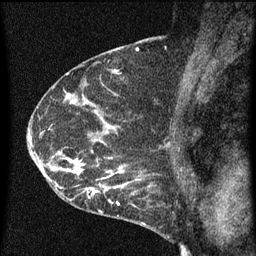
Breast MRI (dynamic contrast-enhanced), one sagittal slice; position 42 of 60 along the scan axis; dynamic contrast-enhanced series, image 2 of 3 at this slice position (ordered by acquisition); 1.5 T; TE 4.2 ms, TR 8 ms; 2 mm slice thickness; 256 × 256 image matrix. Female patient, age 54 years.
Outlined on this slice (semi-automatically segmented with operator editing):
- analysis volume of interest (the breast-tissue region the enhancement analysis was run in; not a lesion): box from (x=49, y=138) to (x=162, y=209) px
- tumour enhancement mask (voxels above the 70 % enhancement threshold inside the analysis volume of interest): (x=49, y=142)–(x=155, y=209)